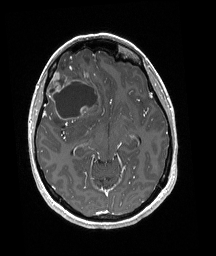
Brain MRI from a brain-tumour surgery series, one axial slice. Position 111 of 192 along the scan axis. T1-weighted post-contrast. 1 mm slice thickness. 216 × 256 image matrix. From the clinical record (not read from this slice): histopathology: Oligodendroglioma; WHO grade: 3; IDH mutation: yes.
Structures marked on this image (manually delineated by an expert):
- tumour: box from (x=45, y=51) to (x=98, y=125) px